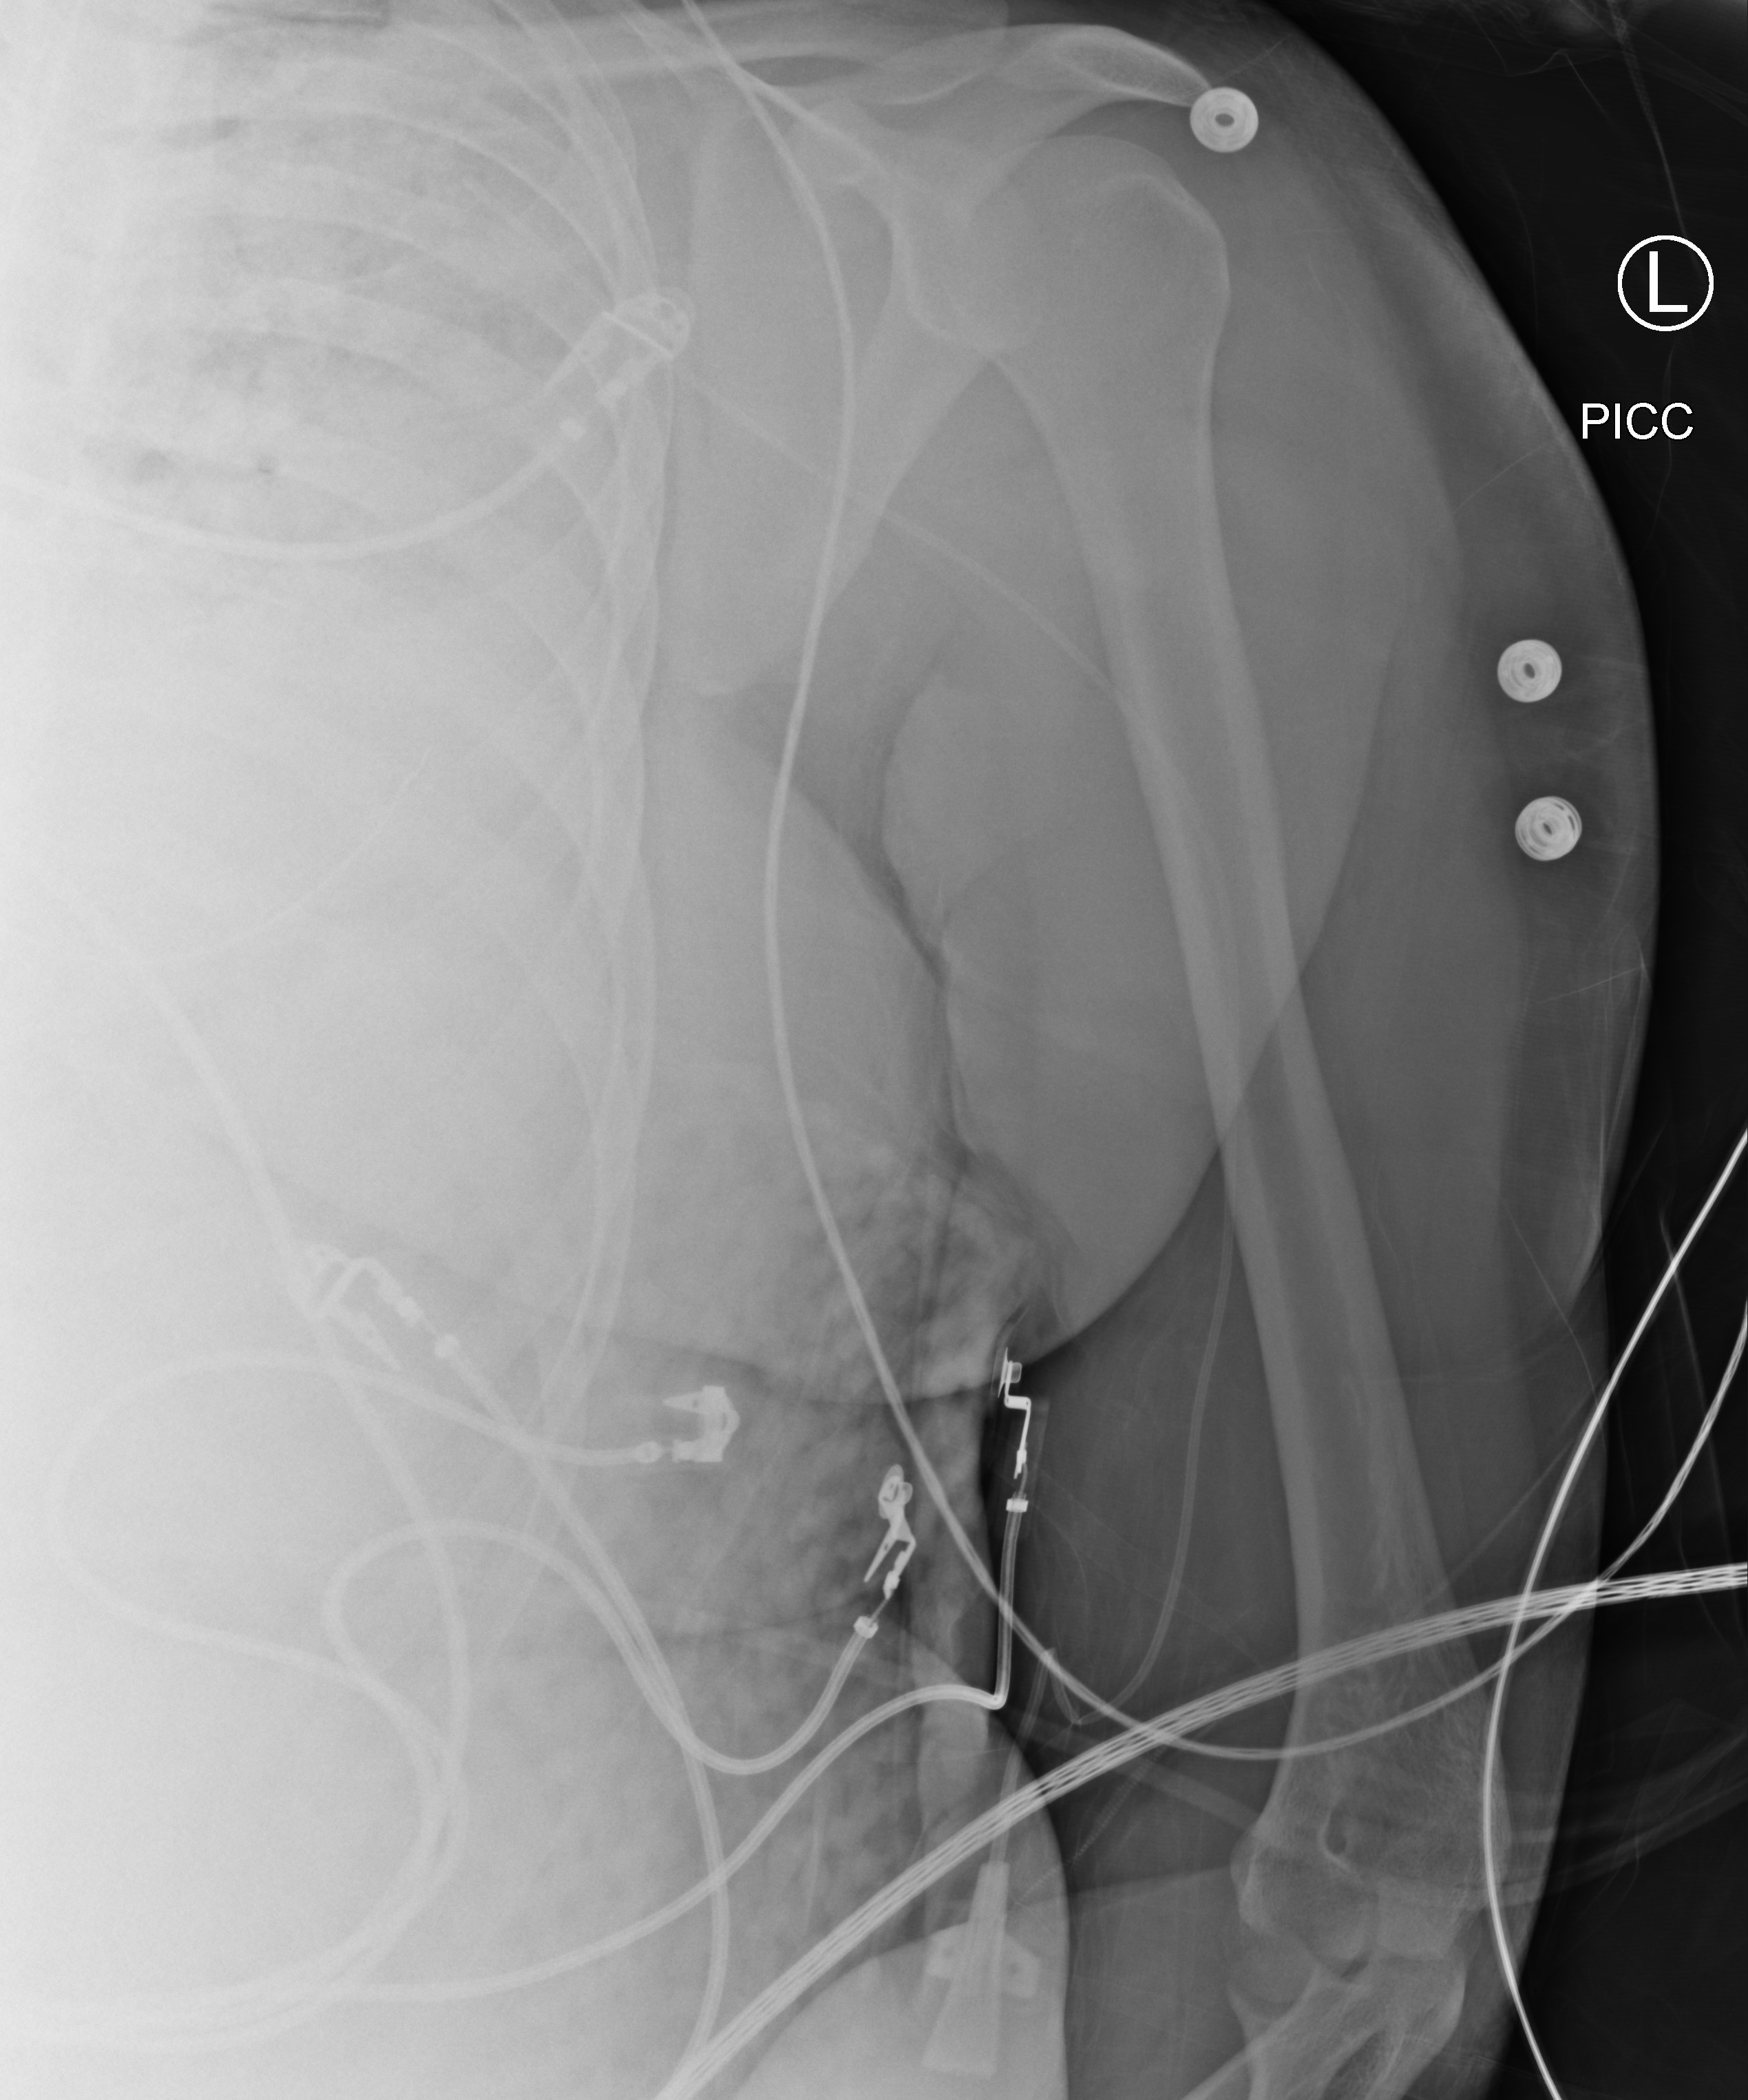
Bedside chest radiograph (computed radiography), anteroposterior (AP) projection. Adult patient hospitalised with COVID-19, age 18–59 years.
Admission-level facts for this patient (not findings on this image; timing relative to this image not recorded): hypertension (admission record): no.